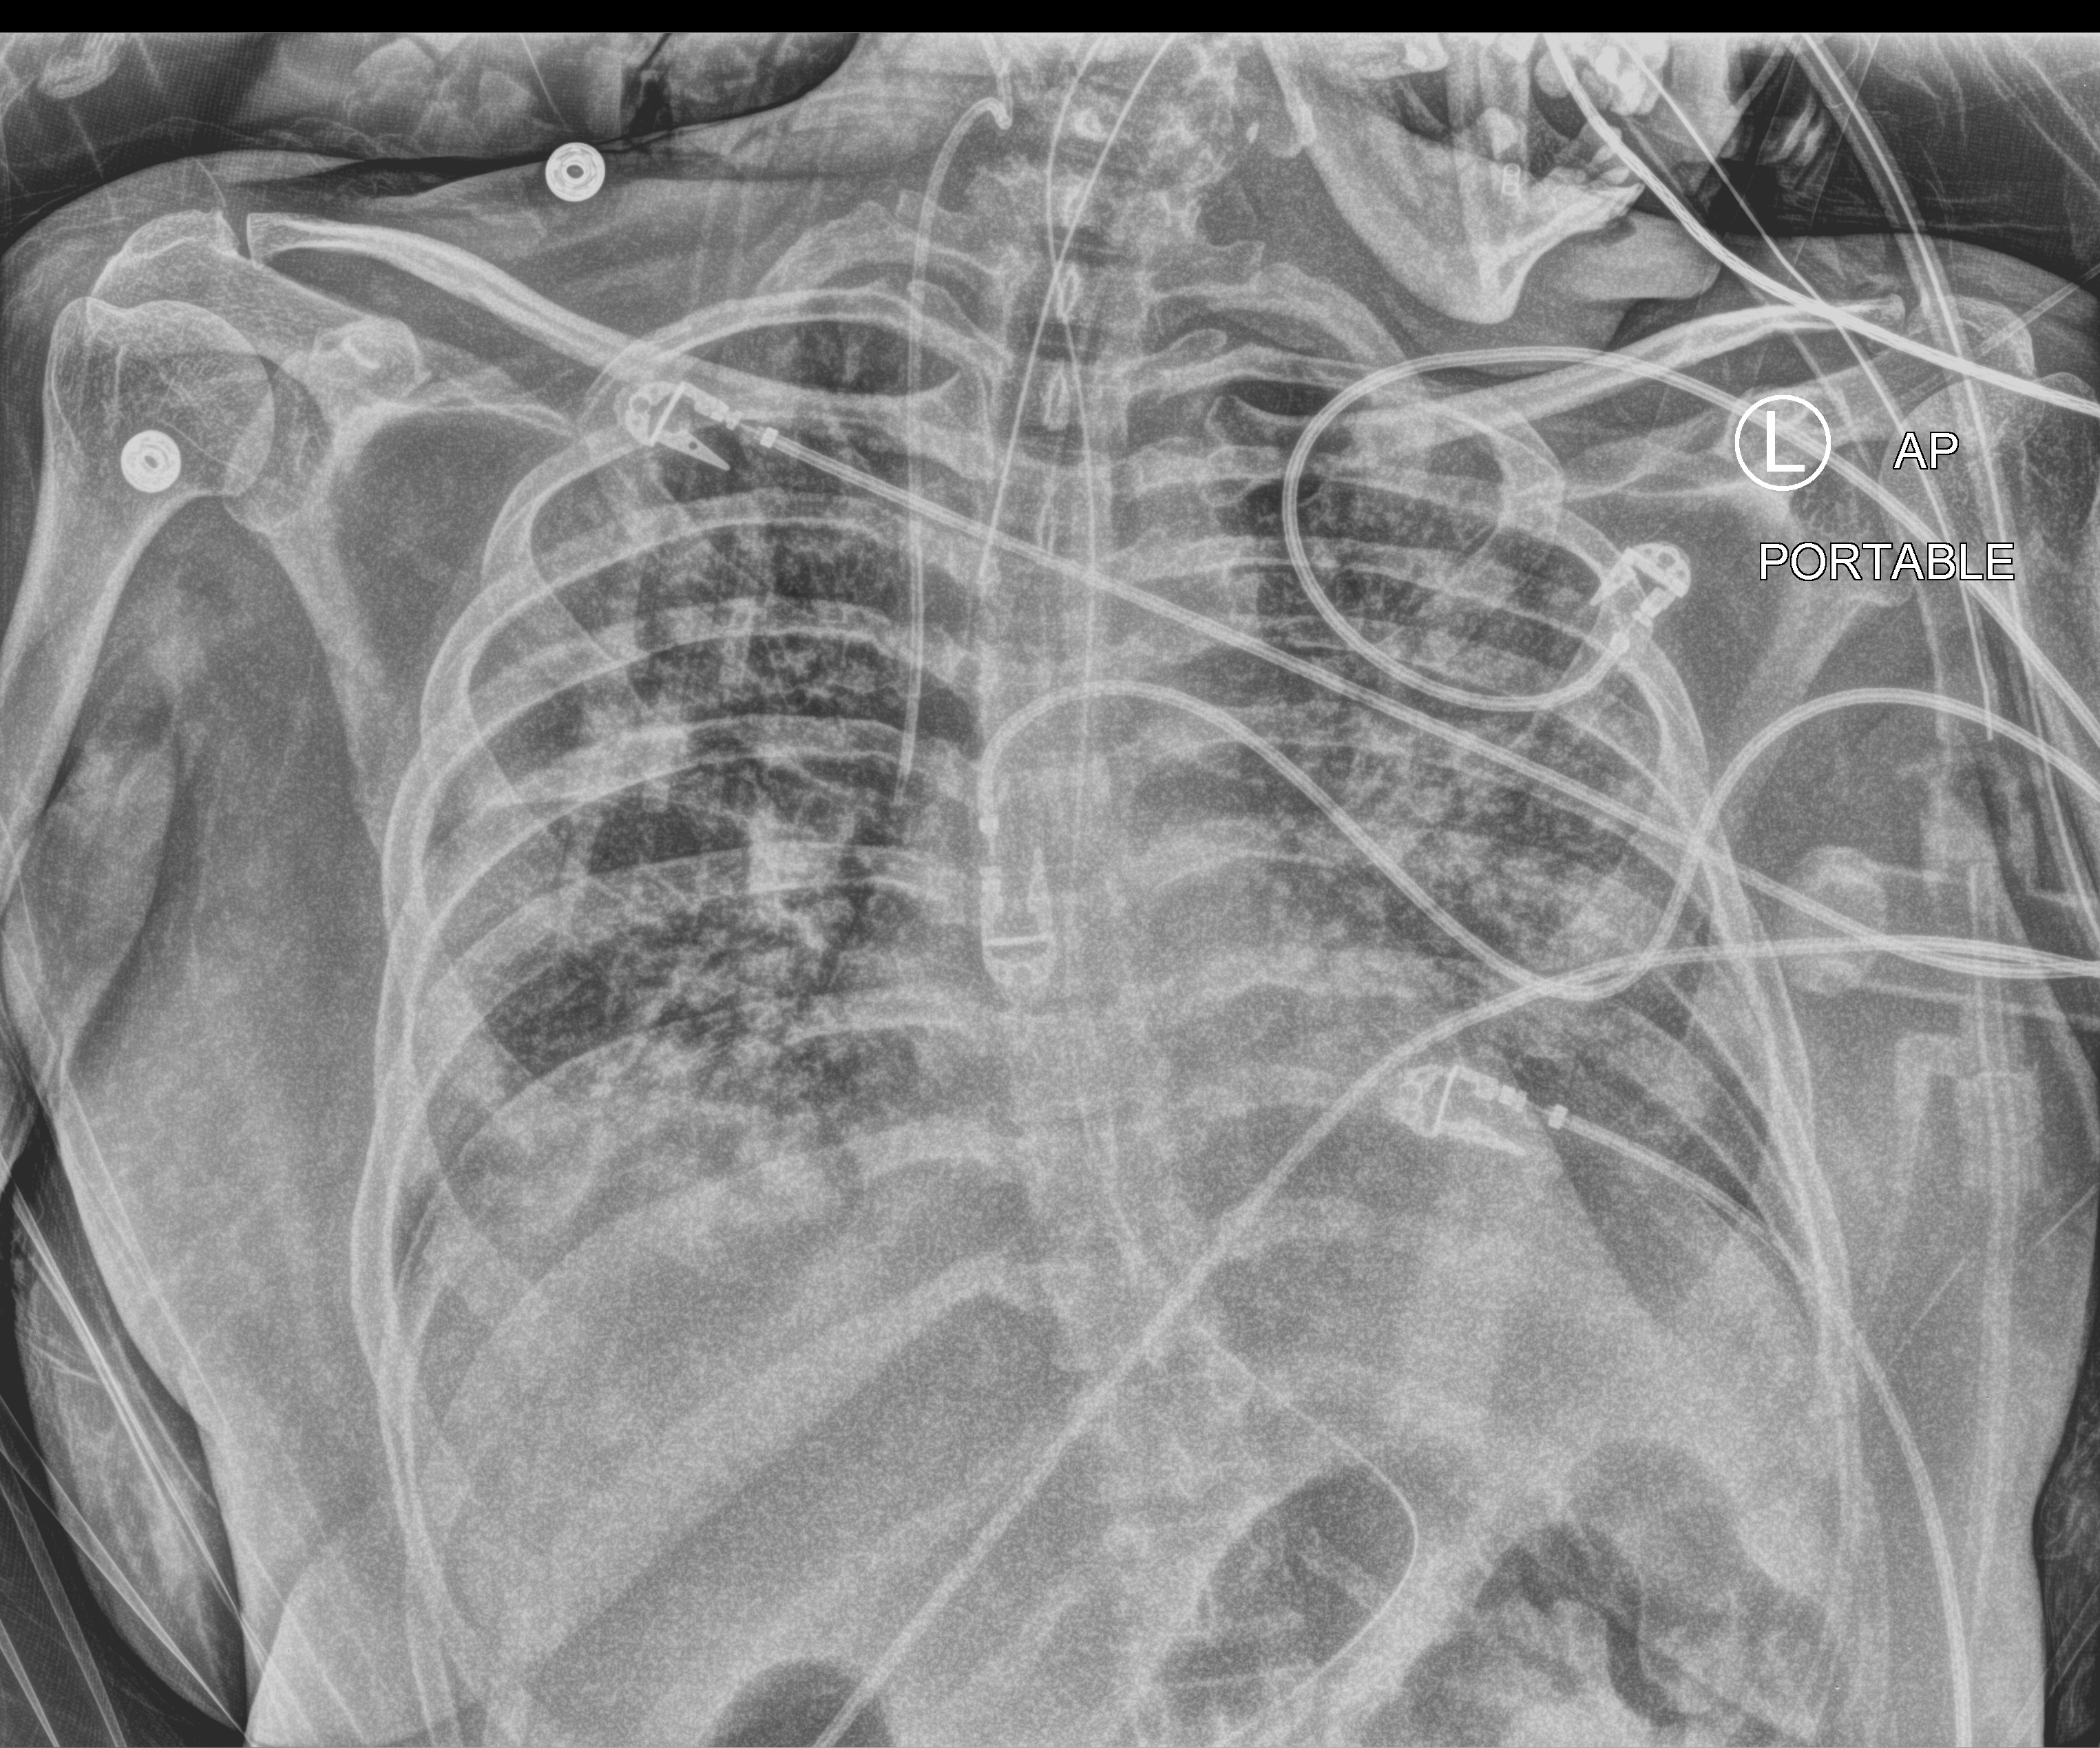
Bedside chest radiograph (computed radiography), anteroposterior (AP) projection. Patient hospitalised with COVID-19, aged 18–59 years.
Hospital-stay facts (about this admission, not read from this image; timing relative to this image not recorded): diabetes (admission record): yes; COPD (admission record): no; smoking status (admission record): never.